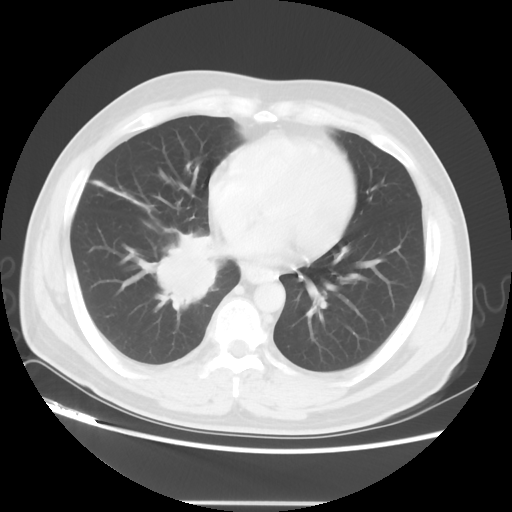
Chest CT, one axial slice; position 18 of 48 along the scan axis; reconstruction kernel STANDARD; 120 kVp; lung window (W 1500 / L -600 HU); 512 × 512 image matrix, field of view 390 × 390 mm. Male patient, age 53 years. Case-level facts recorded for this patient, not image findings: clinical TNM (as recorded): T2 N3 M0; histopathological grade: G3.
Structures marked on this image (rectangle marked by the reading radiologist):
- lung tumour (recorded histology: small cell carcinoma): bounding box [x1, y1, x2, y2] px = [141, 227, 228, 319]